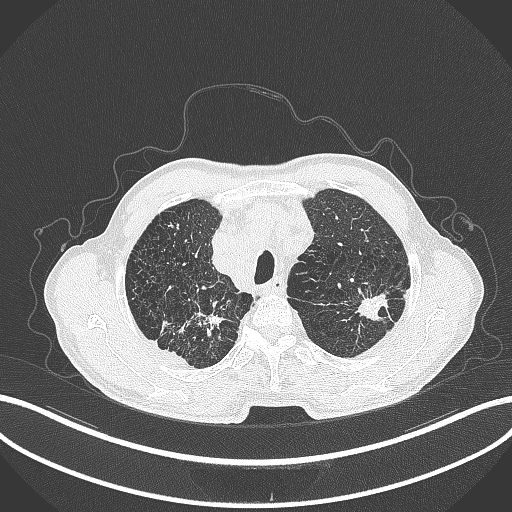
Chest CT, one axial slice. Slice 369 of 463 in the series (ordered by position). Lung window (W 1500 / L -600 HU). 1 mm slice thickness. 512 × 512 image matrix. Patient: male, 74 years. From the clinical record (not read from this slice): clinical TNM (as recorded): T2a N1 M0.
Structures marked on this image (bounding box drawn by a radiologist):
- lung tumour (recorded histology: adenocarcinoma): bounding box <354,294,392,322> (left, top, right, bottom; pixels)